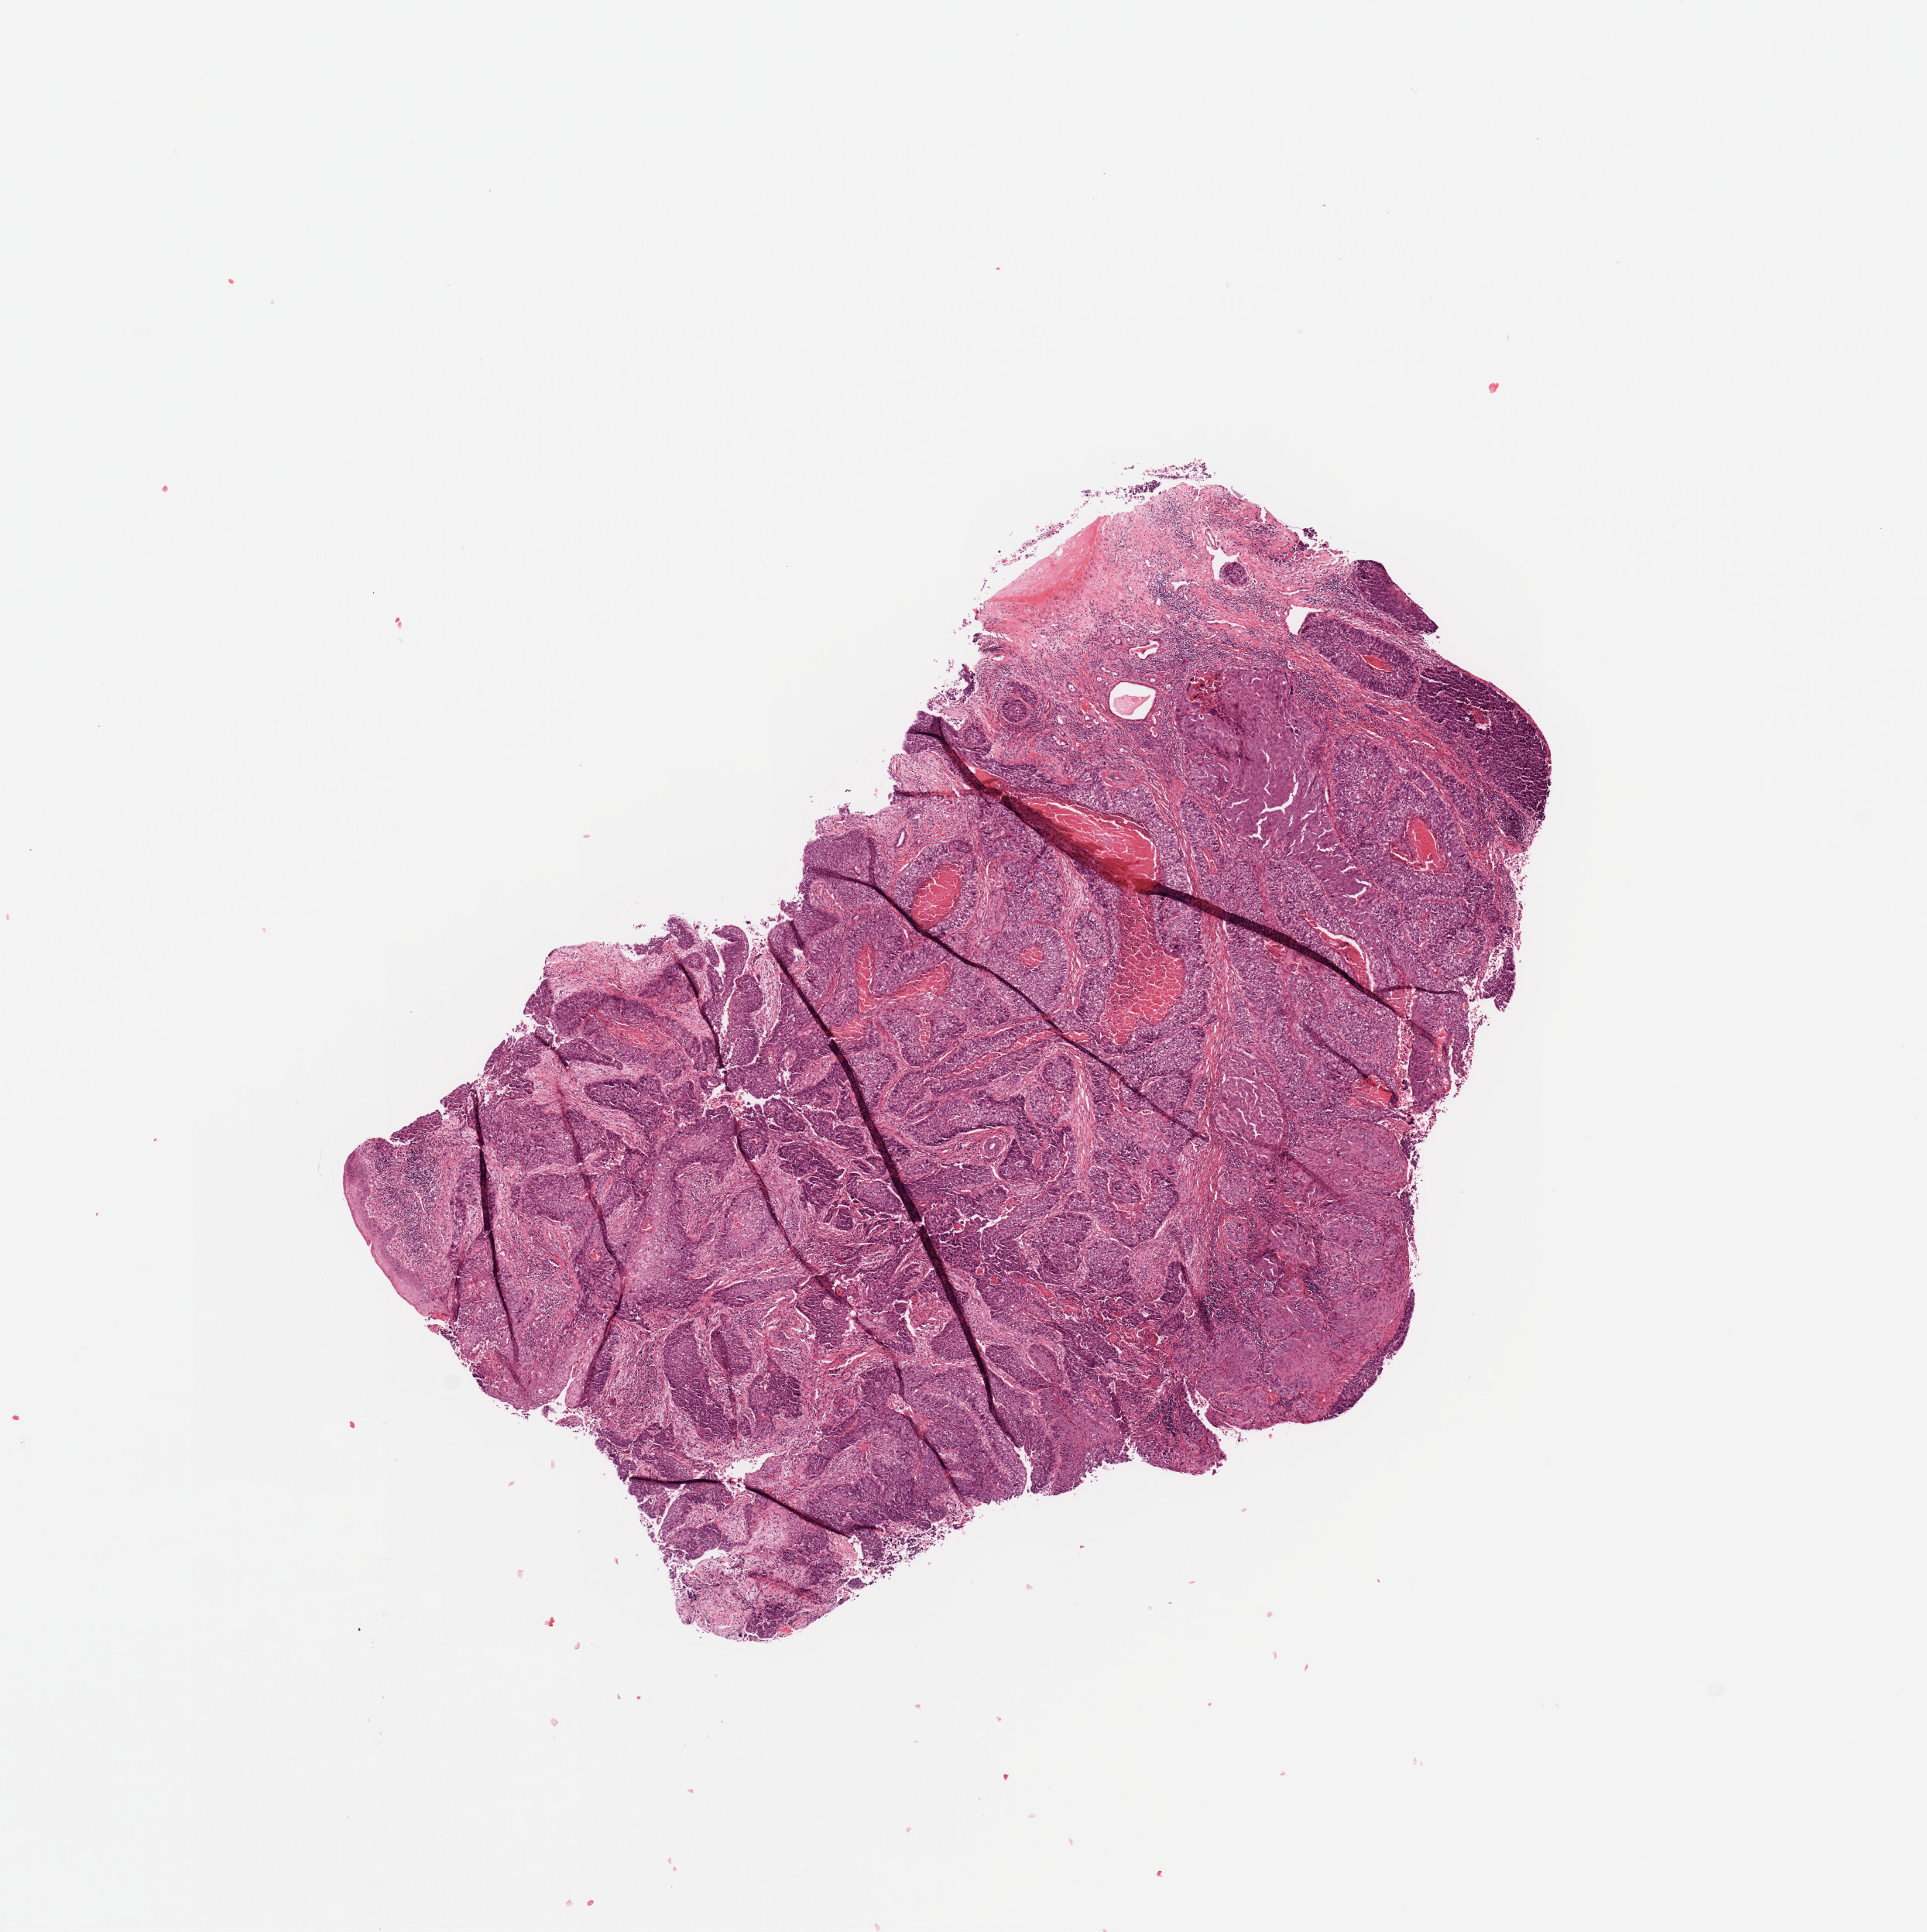
Digitized Hematoxylin and eosin (H&E) stained tissue section (whole slide) — low-resolution overview of the scanned area, about 9.8 x 9.9 mm (slide scanned at 20x). Head and neck, tissue type not recorded. Patient: female, age 63 years.
* patient diagnosis: Squamous cell carcinoma, NOS (larynx, NOS)